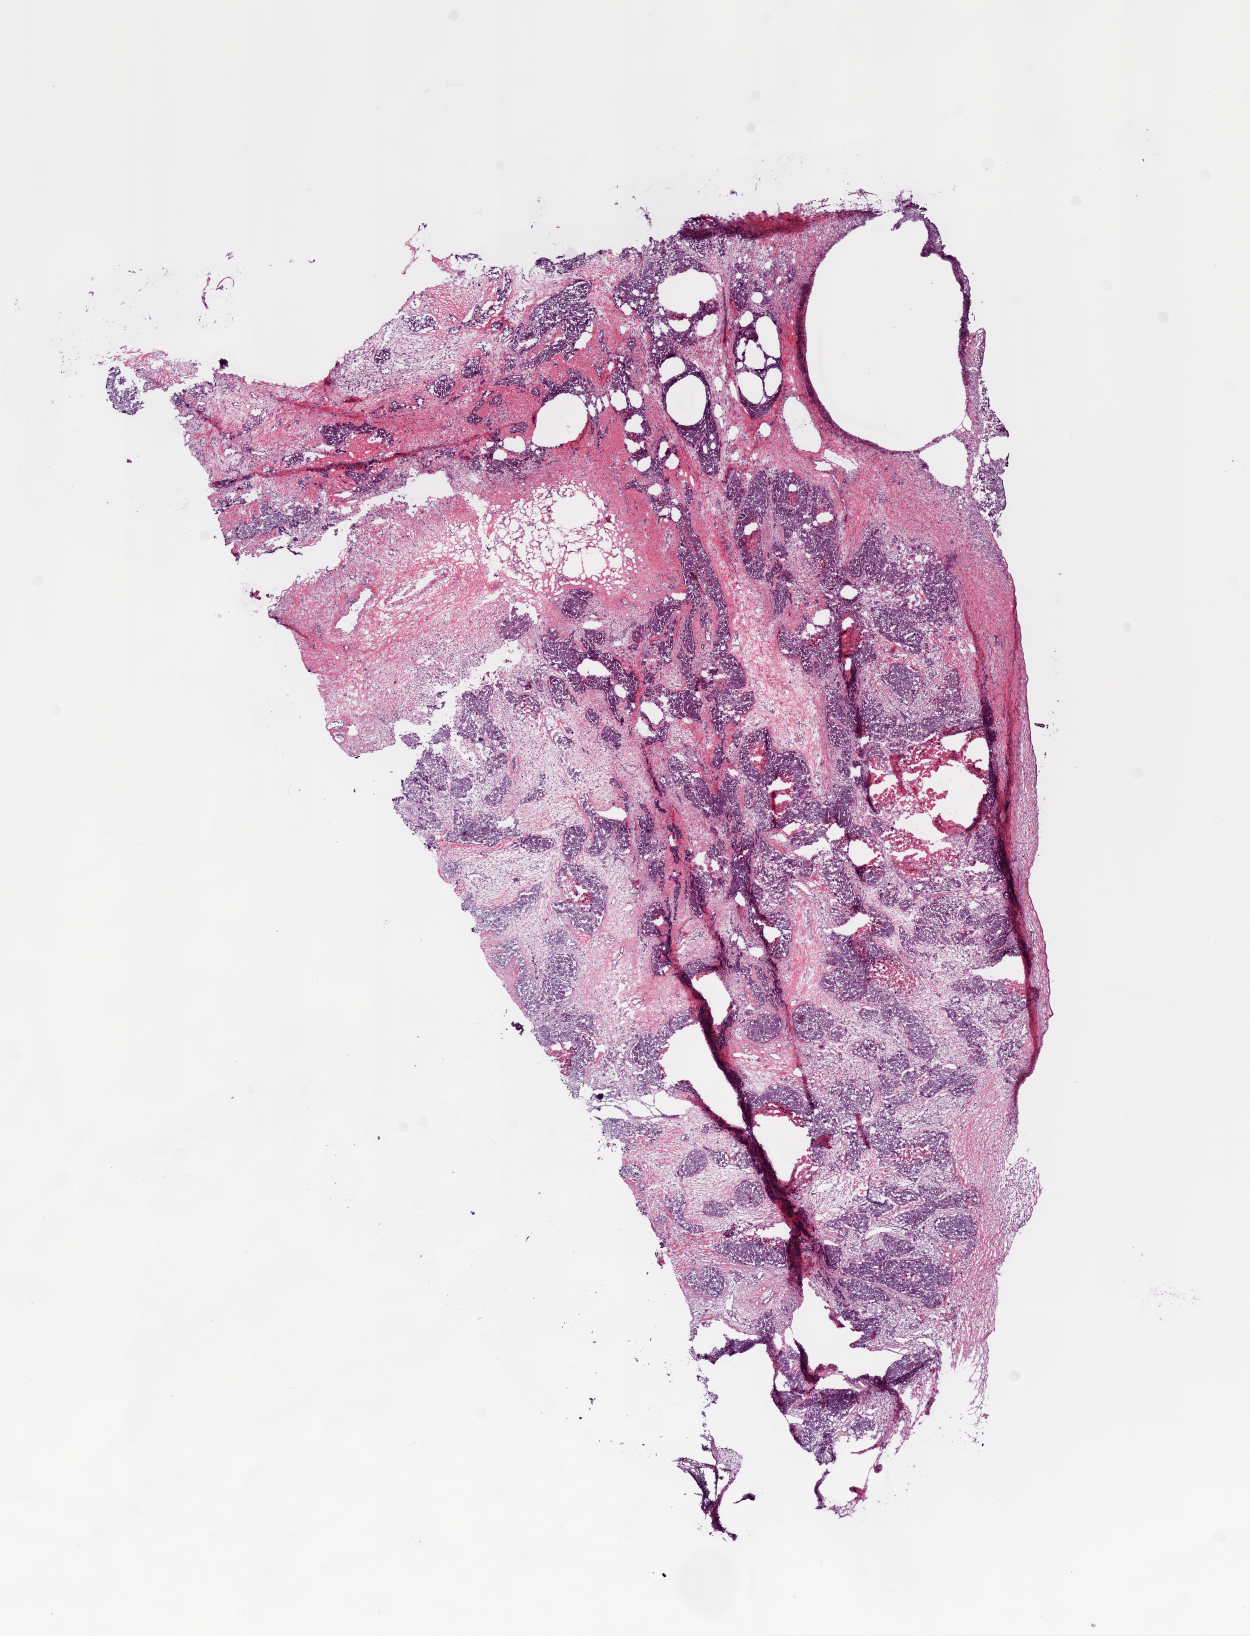
H&E-stained whole-slide image, low-resolution overview of the scanned area, about 10.0 x 13.1 mm (acquisition: 20x scan). Frozen section from the bottom of the tissue portion. Ovary, primary tumour sample. Female, age 52 years at initial diagnosis. Histologic grade: G3 (poorly differentiated). Slide review estimates, as recorded: tumour cells 70%, tumour nuclei 80%, normal cells 0%, stromal cells 20%, necrosis 10%.
- histologic diagnosis: Serous cystadenocarcinoma, NOS
- FIGO stage: IIIC